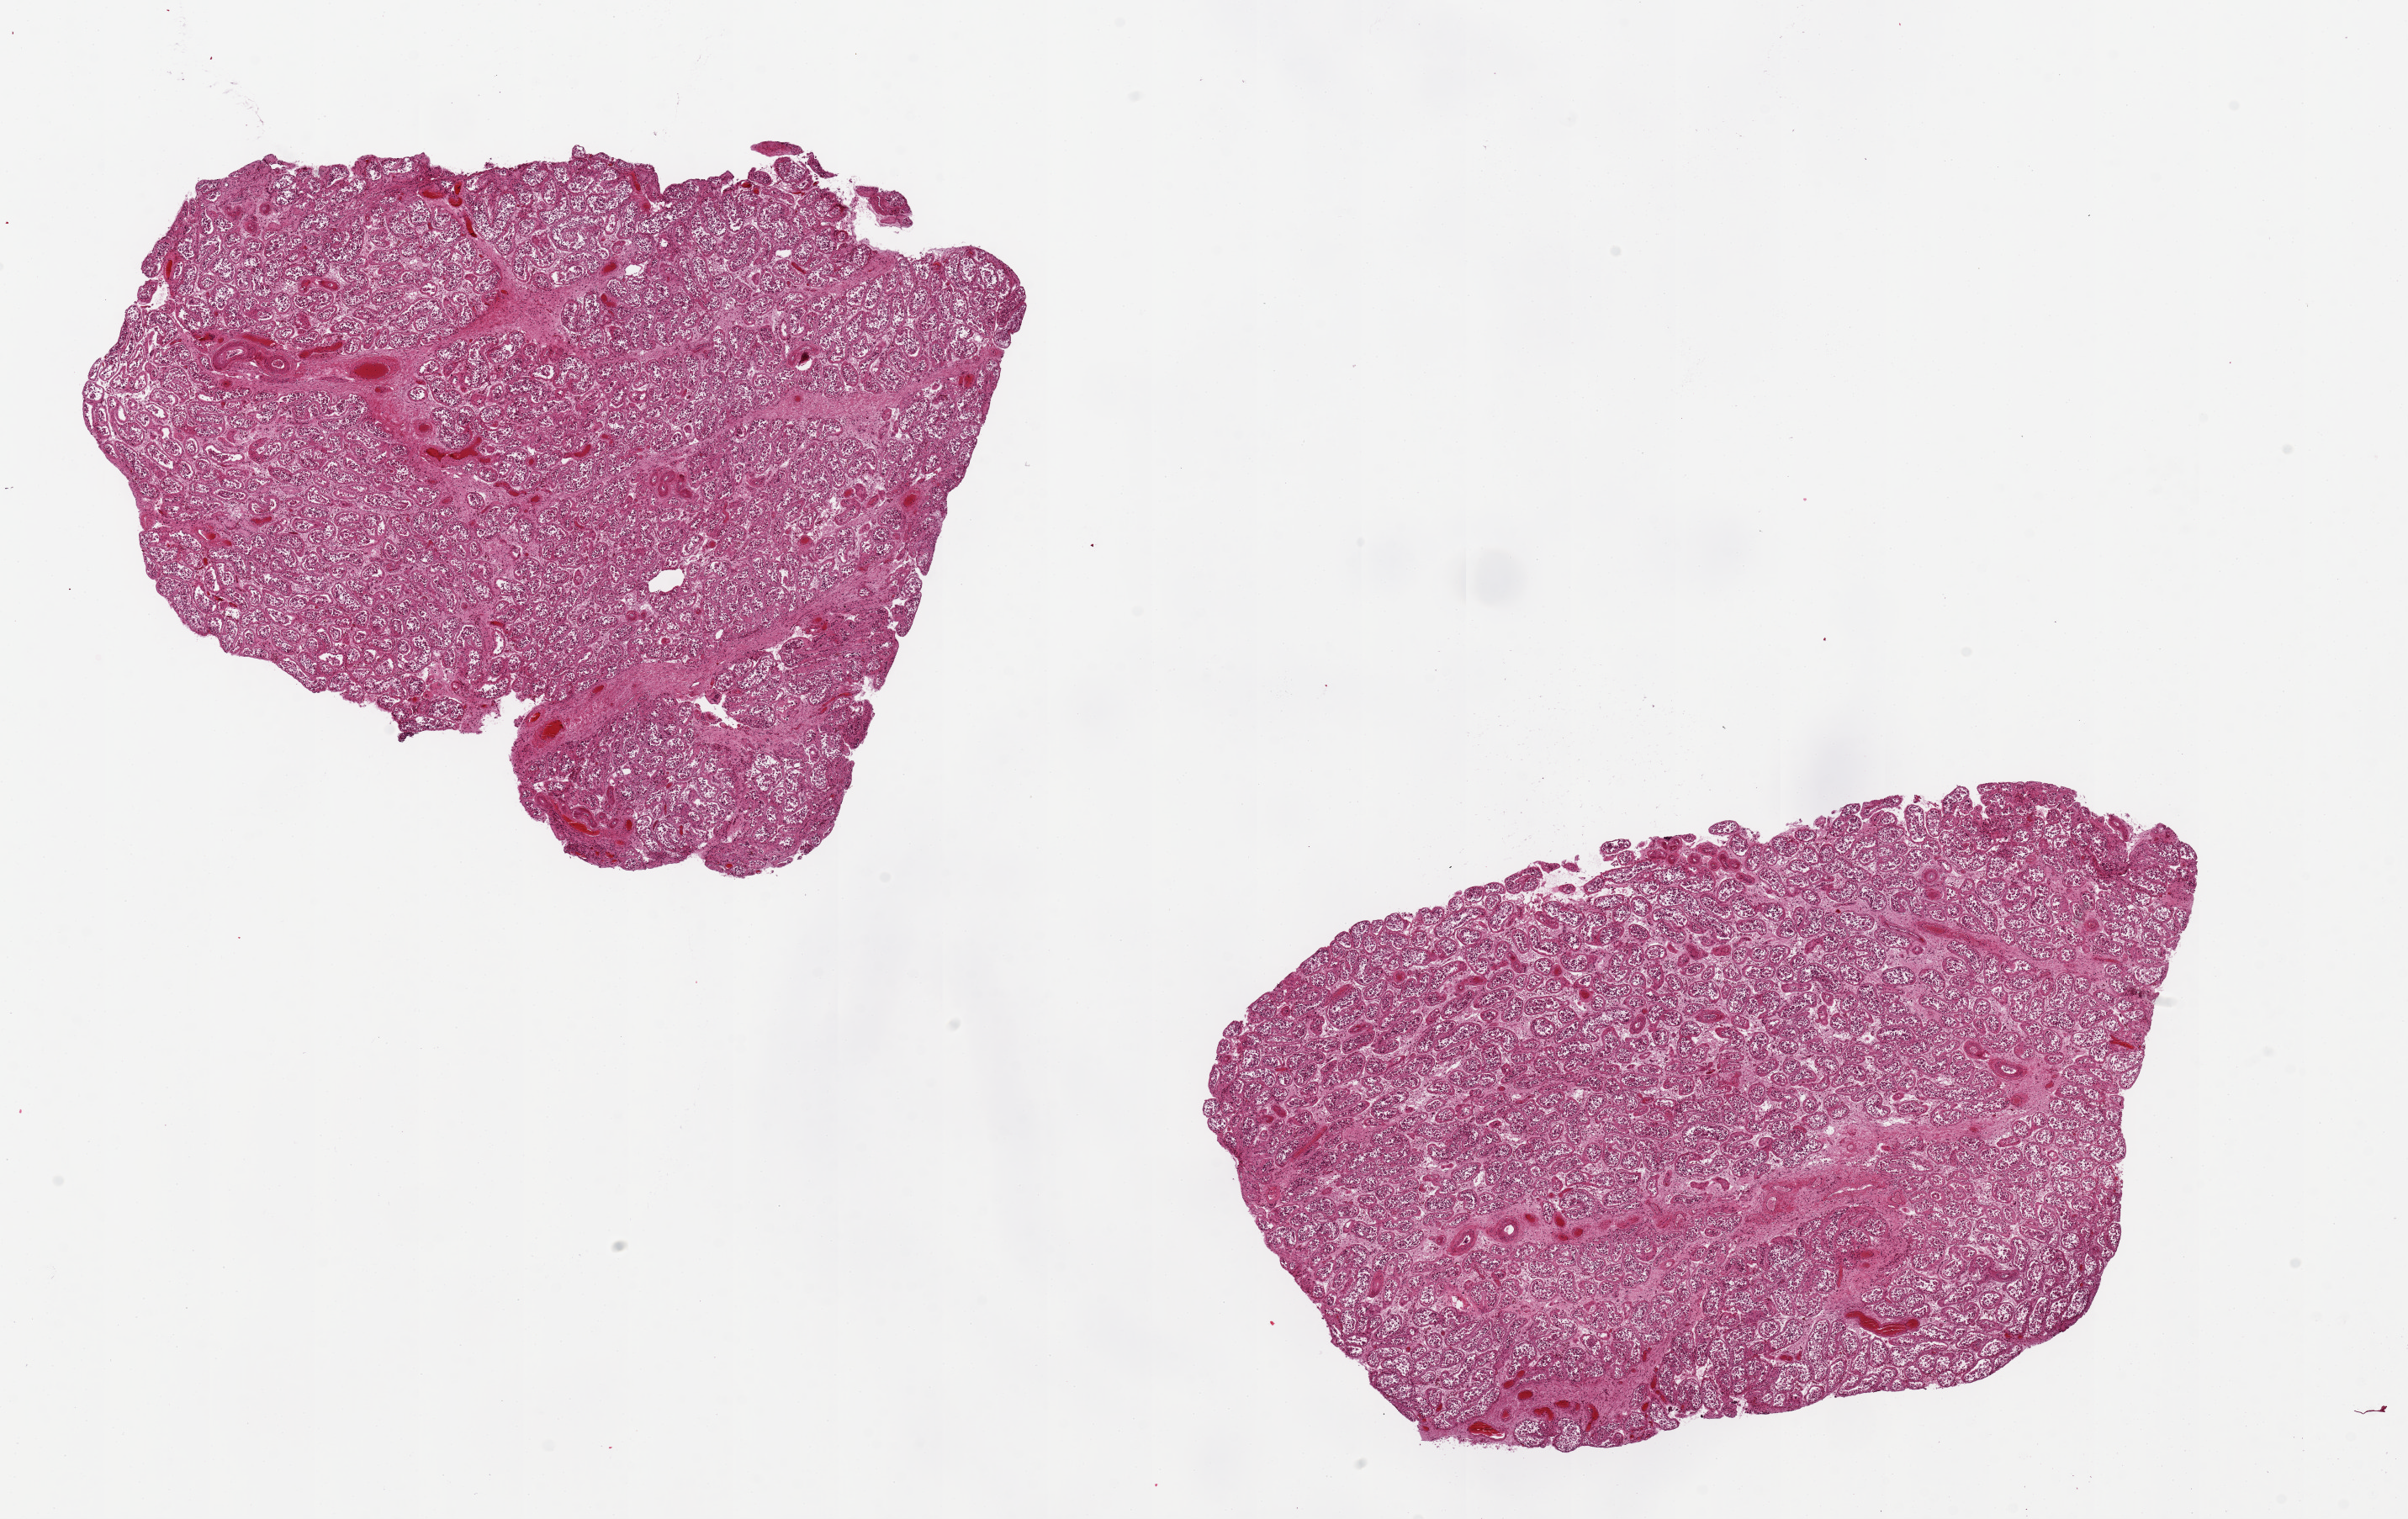
Hematoxylin and eosin (H&E) whole-slide image — whole scanned area (about 22.6 x 14.3 mm) shown as a low-resolution overview; PAXgene-fixed paraffin-embedded (PFPE) section; target tissue: testis; tissue donor sample.
• pathologist's review note for this sample: 2 pieces 9x5 & 8x6 mm; slightly reduced spermatogenesis